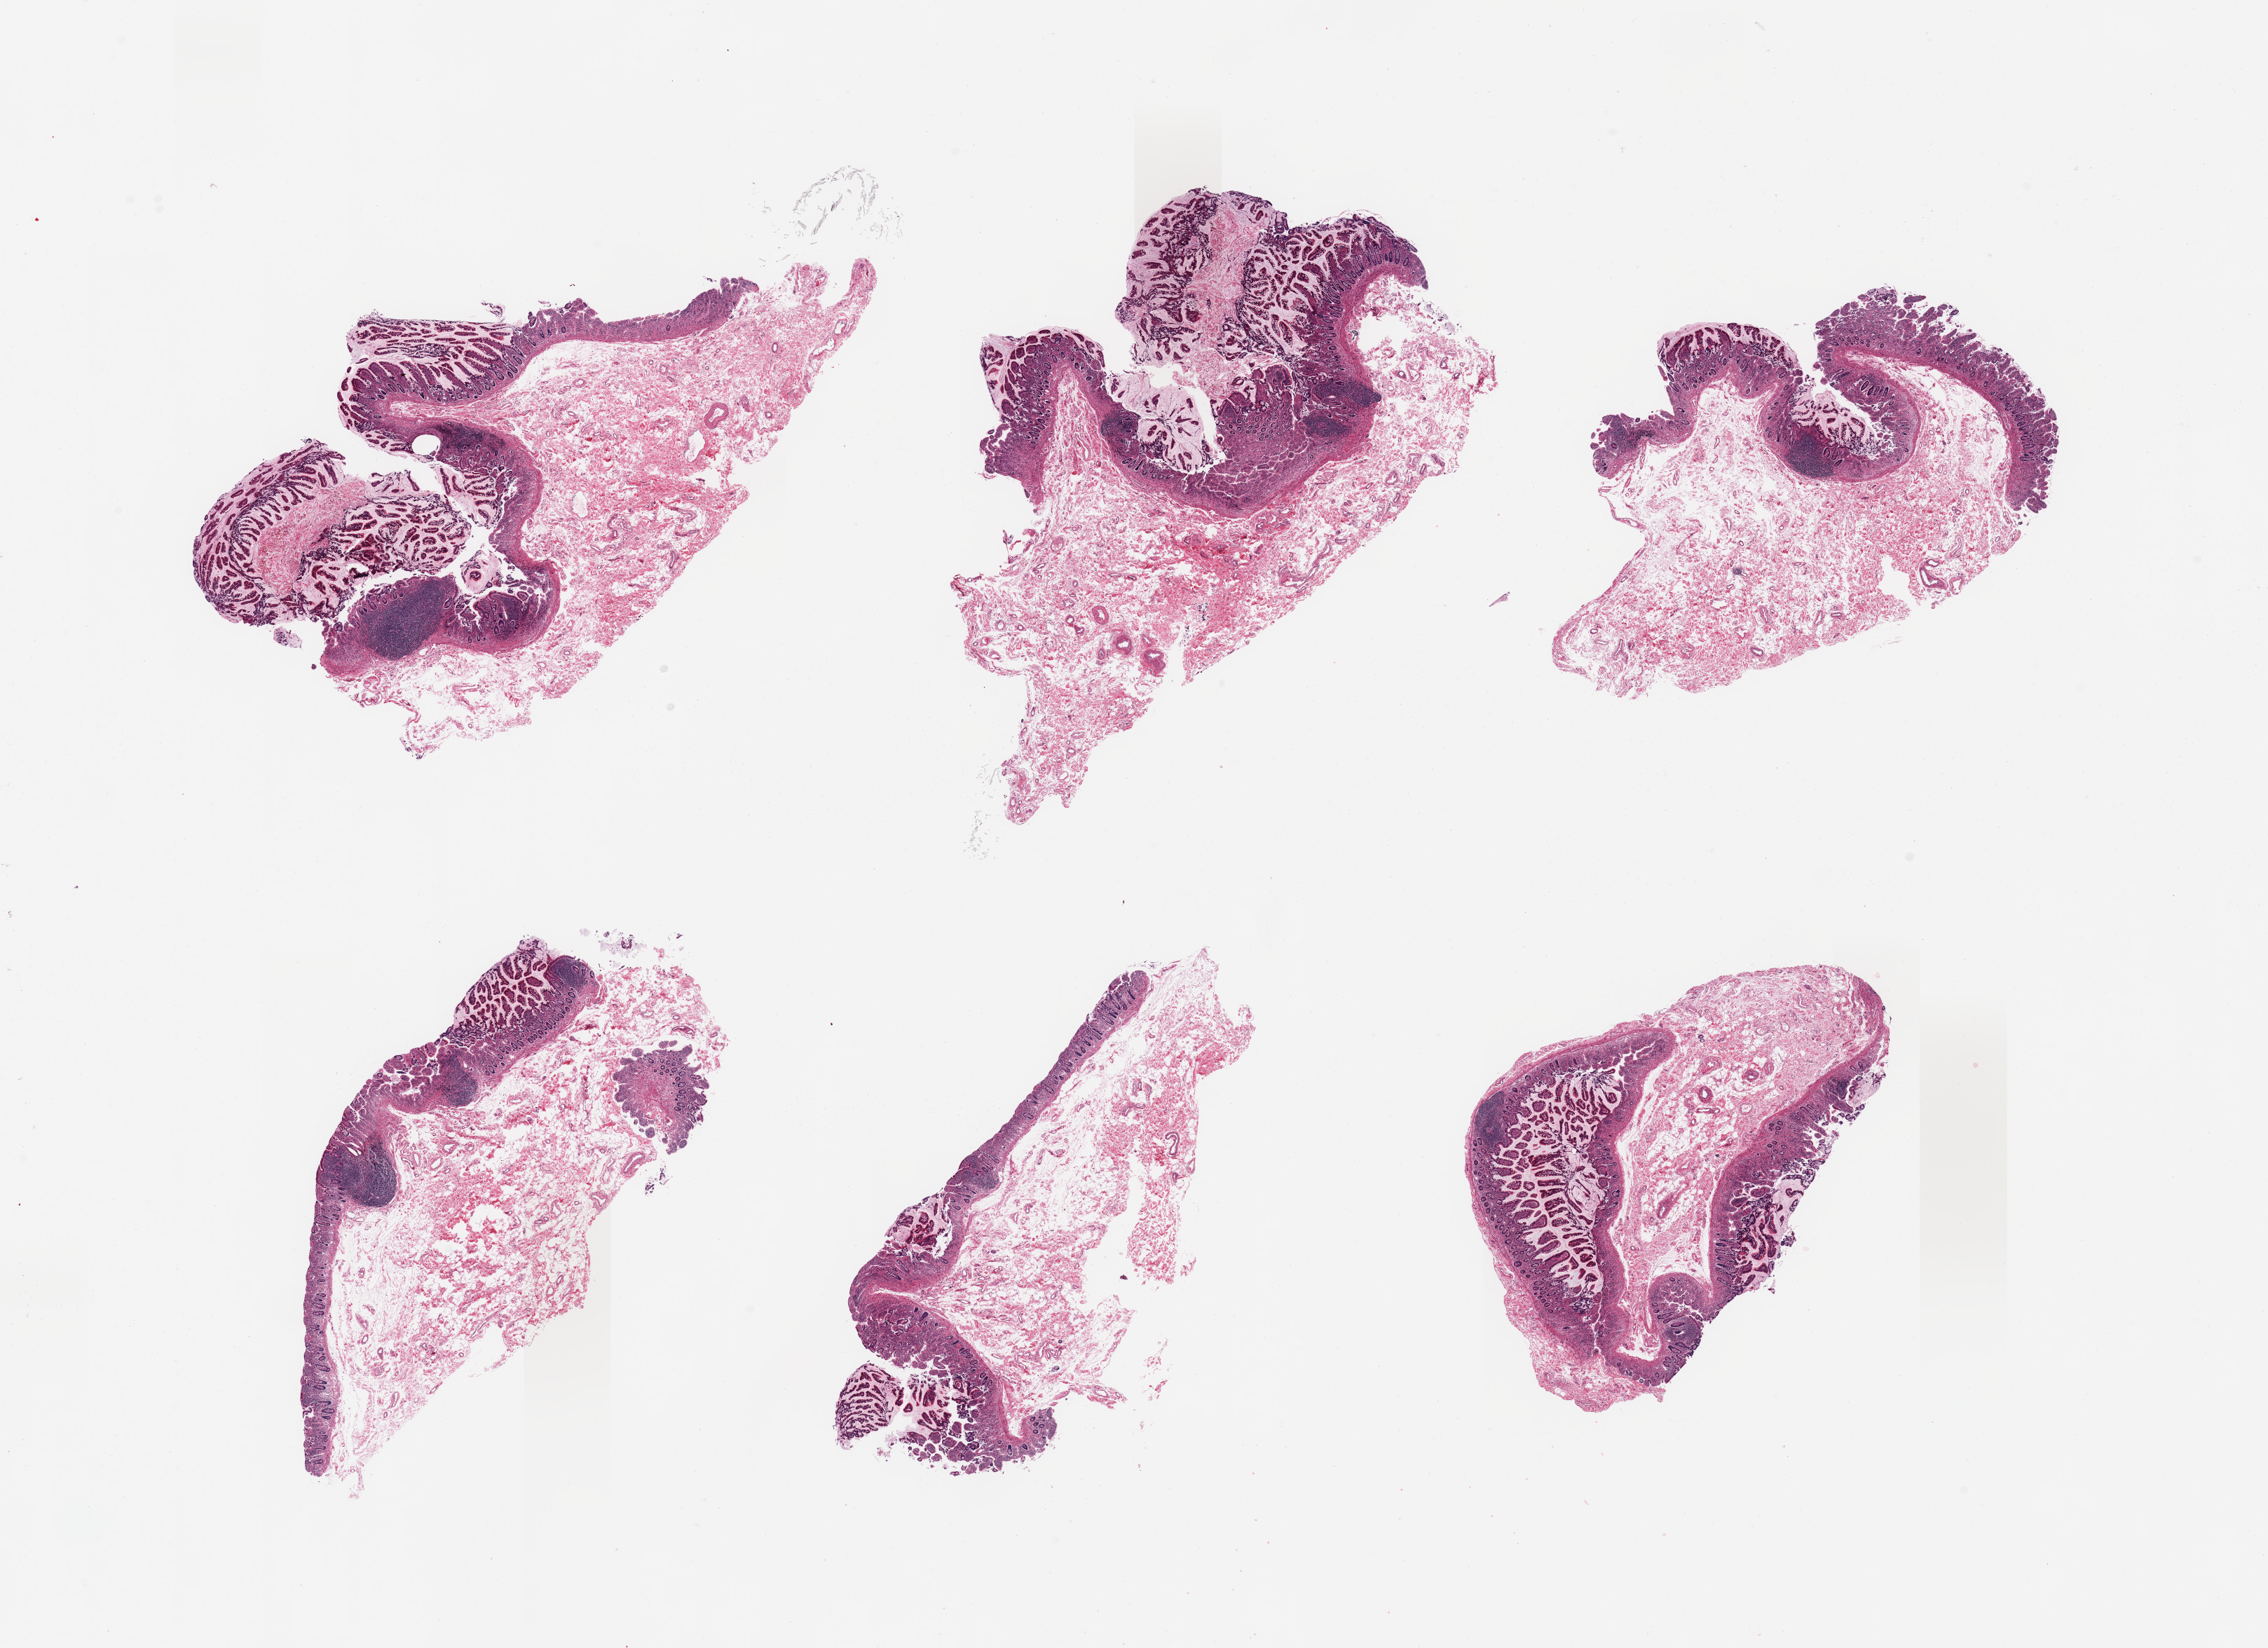
Digitized hematoxylin and eosin (H&E)-stained section, brightfield — whole scanned area (about 25.6 x 18.6 mm, acquisition: 20x scan) shown as a low-resolution overview; PAXgene-fixed, paraffin-embedded tissue; section of ileum (target tissue); donor tissue sample.
• review note (as recorded): 6 piece; moderately autolyzed mucosa; residual target lymphoid aggregates are over 25% of tissue